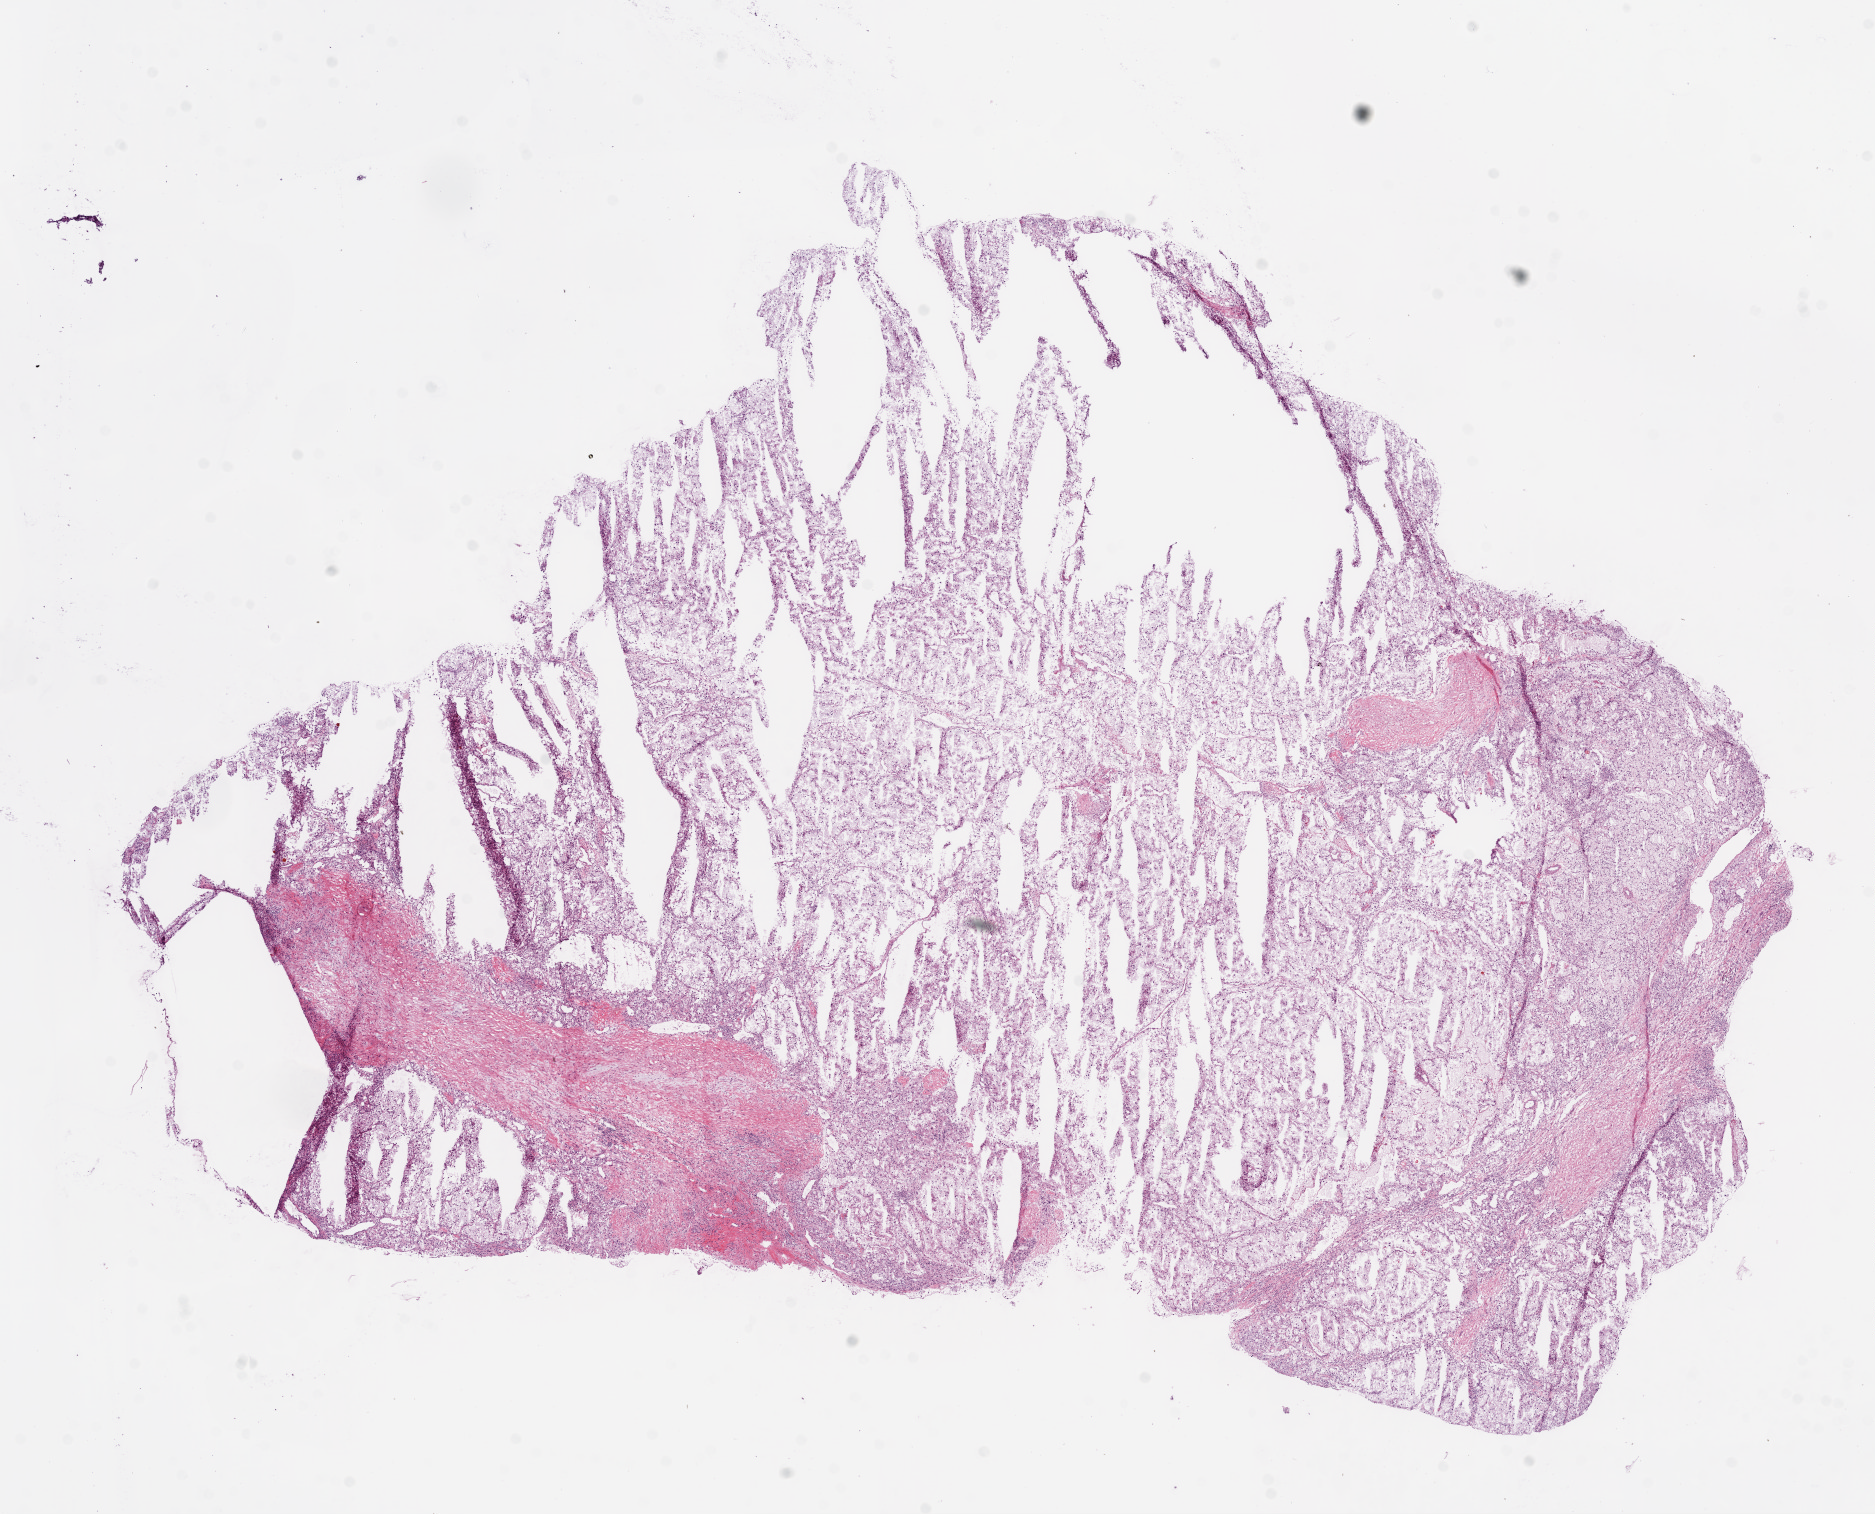
Whole-slide histology image, H&E, whole scanned area (about 15.0 x 12.1 mm) shown as a low-resolution overview. Frozen section from the bottom of the tissue portion. Sample: primary tumour, kidney. Patient: male, age at initial diagnosis 34 years. Histologic grade: G3 (poorly differentiated). Pathologist review of this section (percent, as recorded): tumour cells 100%, tumour nuclei 95%, normal cells 0%, stromal cells 0%, necrosis 0%.
Pathologic diagnosis: Clear cell adenocarcinoma, NOS. AJCC pathologic stage: III. Lymph nodes positive (case pathology): 0 of 5 examined. Laterality: right.